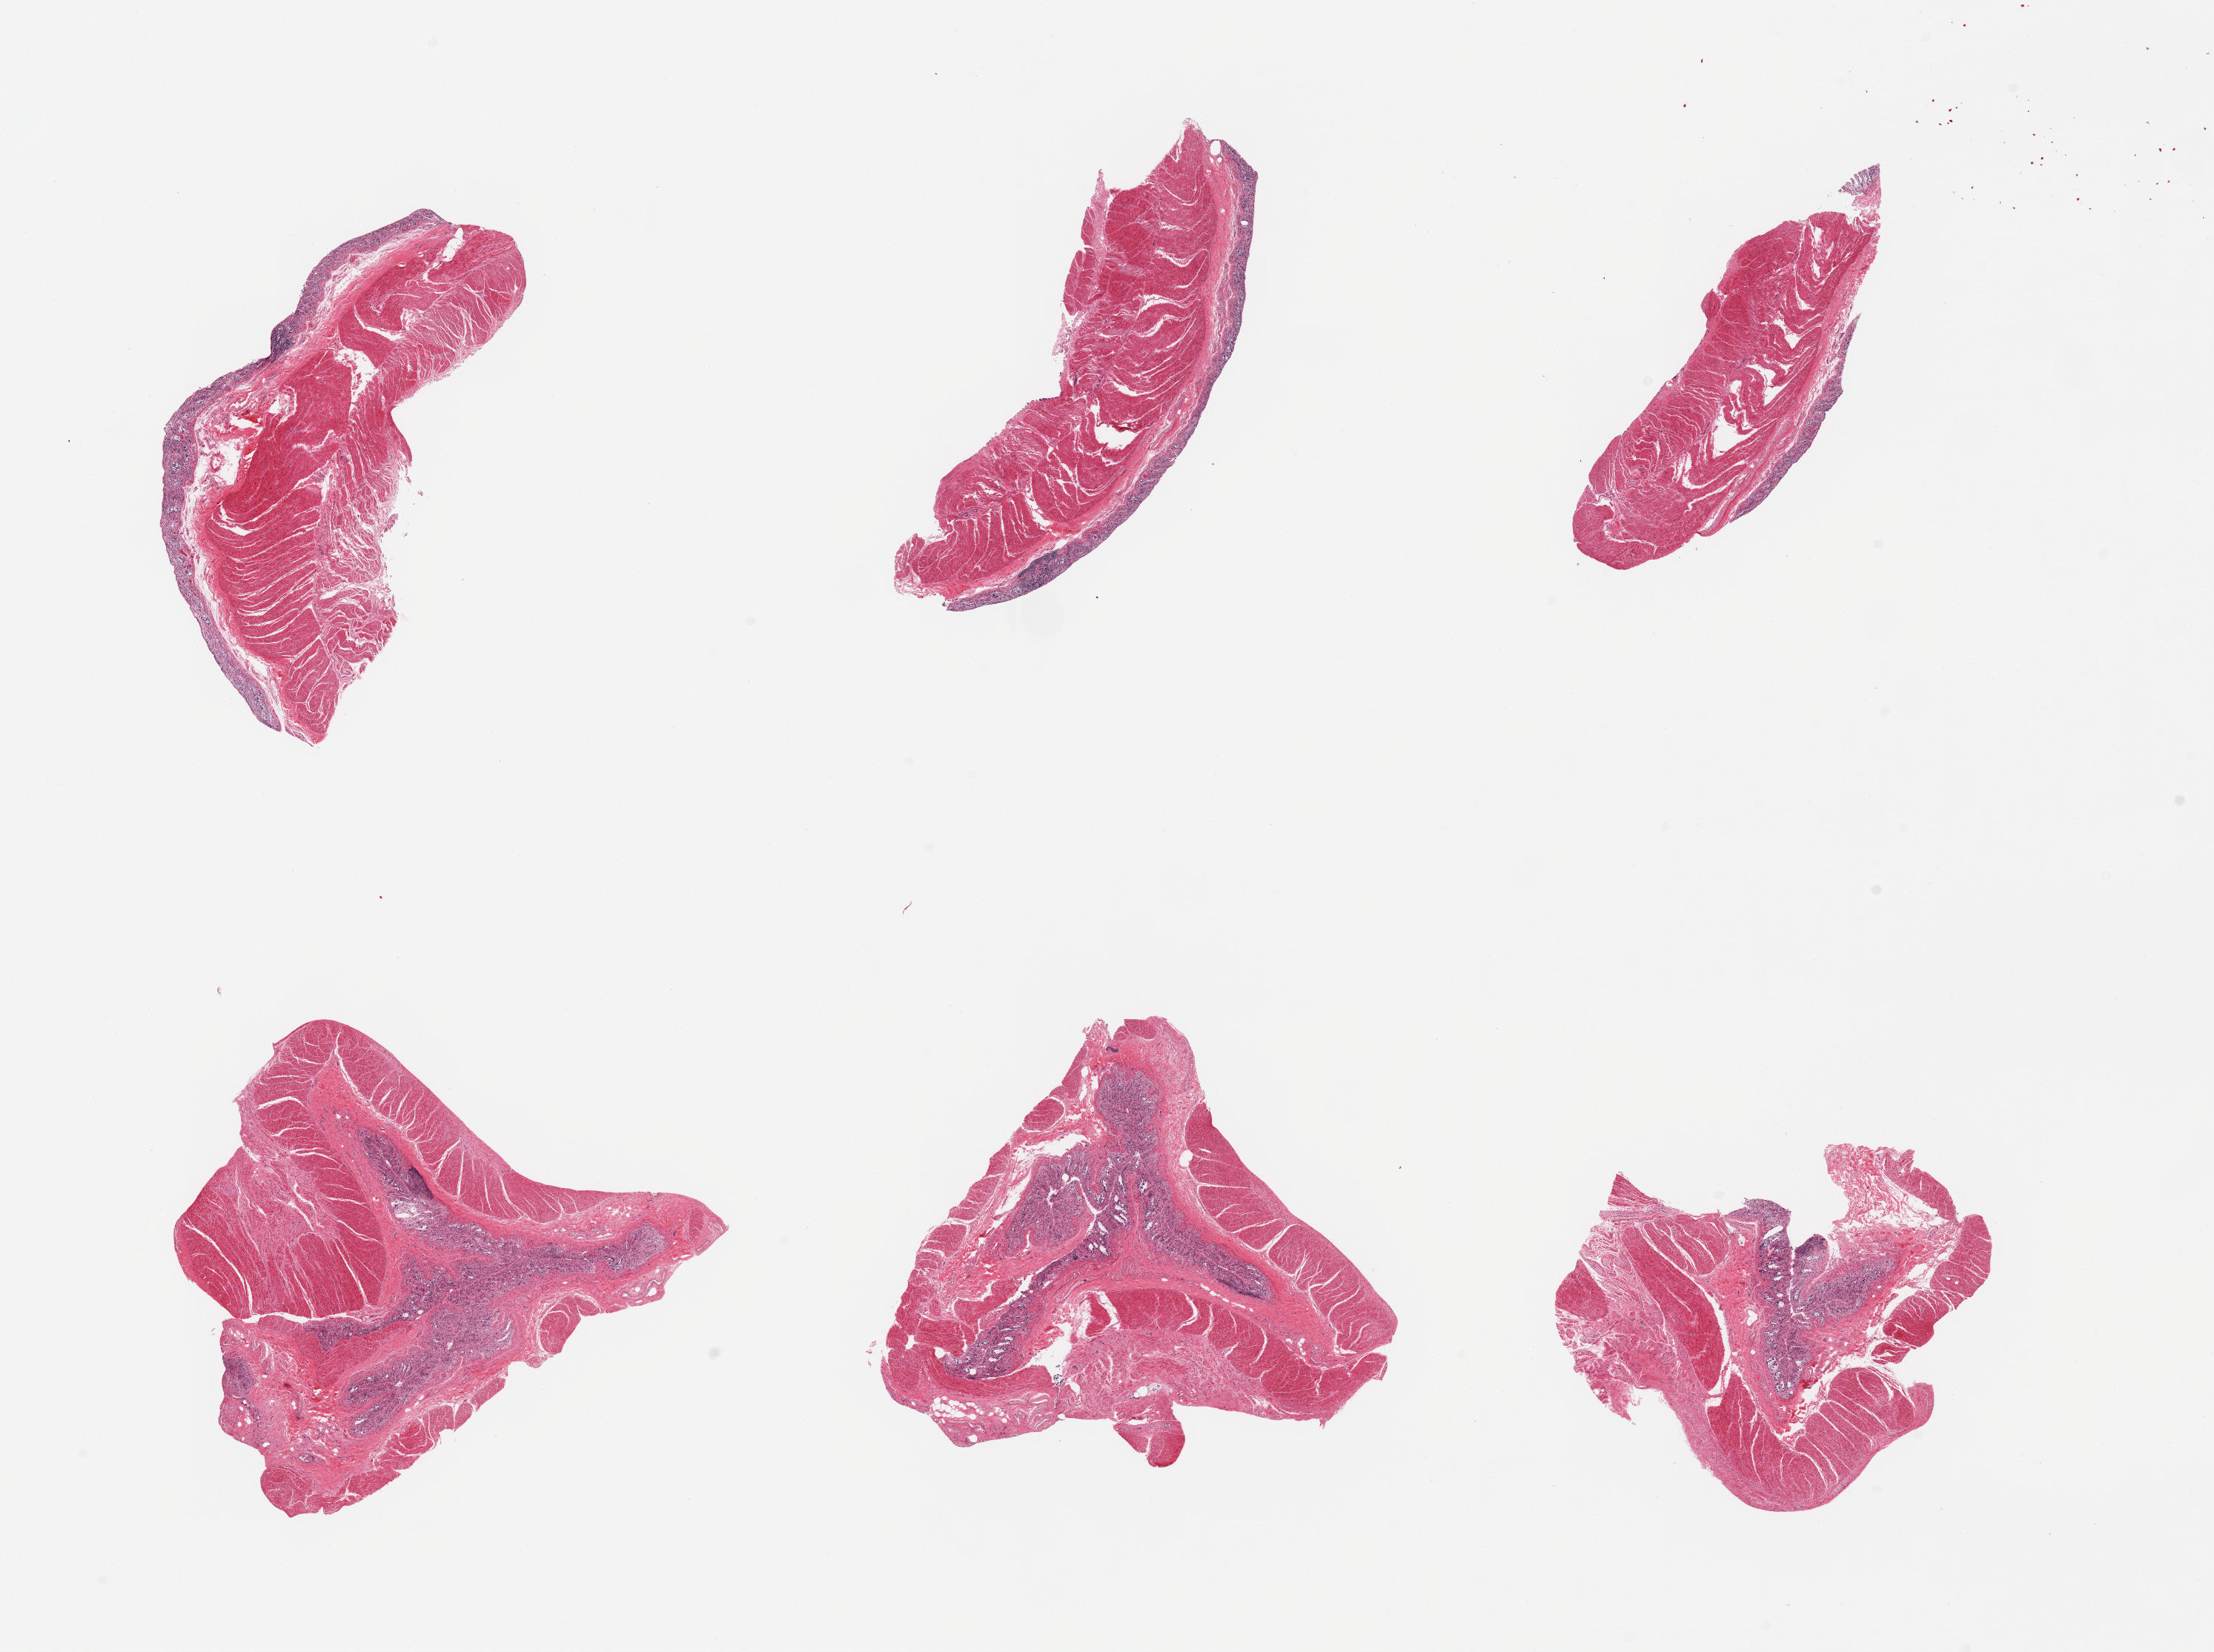
Digitized hematoxylin and eosin (H&E)-stained section, shown as a low-resolution overview of the whole scanned area (about 23.6 x 17.6 mm, acquisition: 20x scan). Male donor.
• specimen: PAXgene-fixed, paraffin-embedded tissue; target tissue: sigmoid colon; tissue donor sample